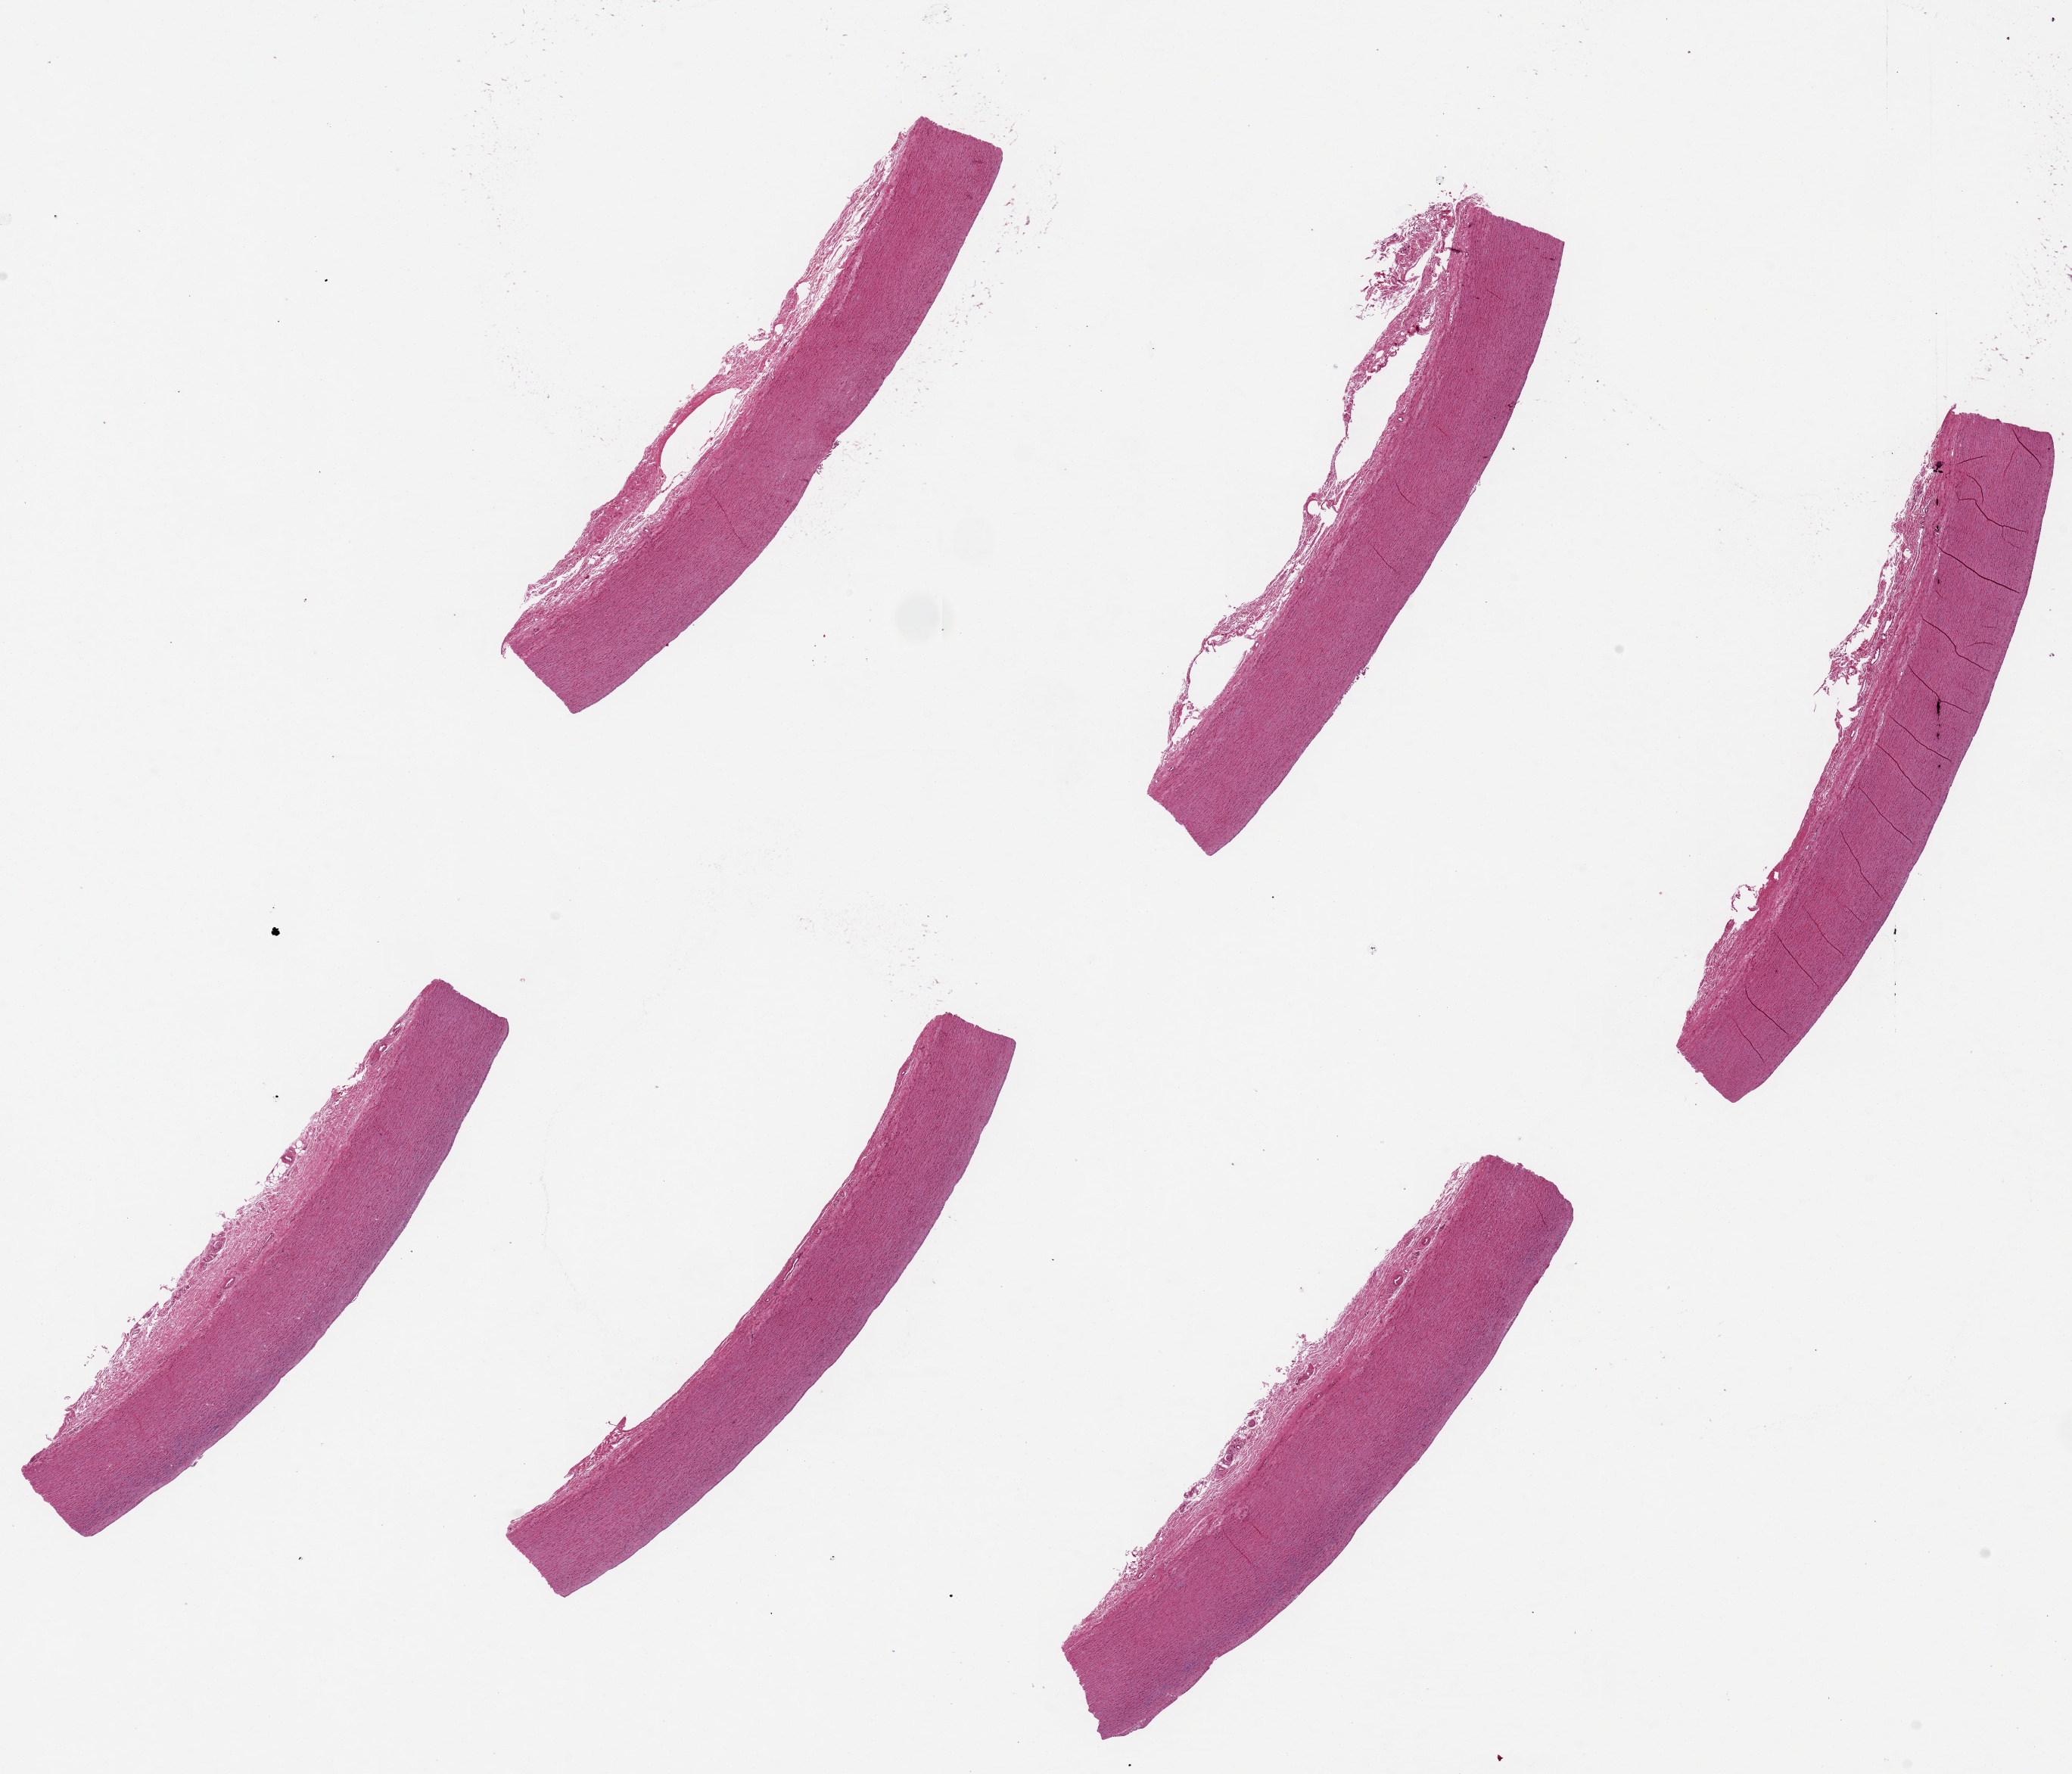
H&E whole-slide image, a low-resolution overview of the entire scanned area, about 21.7 x 18.5 mm (acquisition: 20x scan); PAXgene-fixed, paraffin-embedded tissue; target tissue: aorta; tissue donor sample. Donor sex: female.
* pathologist's review note for this sample: 6 pieces ~7x1.5mm, minimal athersclerosis